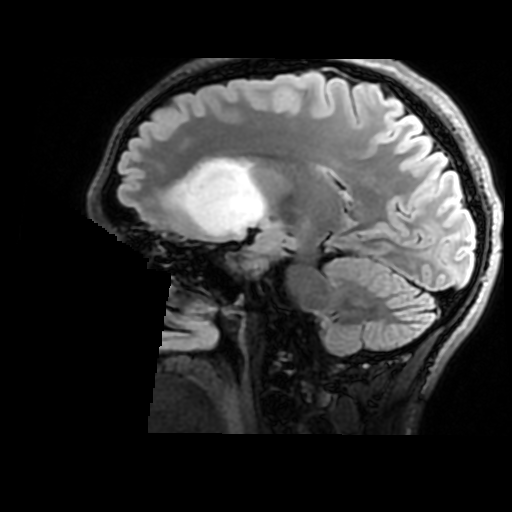
Brain MRI from a brain-tumour surgery series, one sagittal slice; position 103 of 176 along the scan axis; T2 FLAIR; 1 mm slice thickness; 512 × 512 image matrix, field of view 240 × 240 mm. Case-level facts recorded for this patient, not image findings: histopathology: Astrocytoma; WHO grade: 2; IDH mutation: yes.
Outlined on this slice (manually delineated by an expert):
- tumour: bounding box [x1, y1, x2, y2] px = [172, 158, 266, 235]